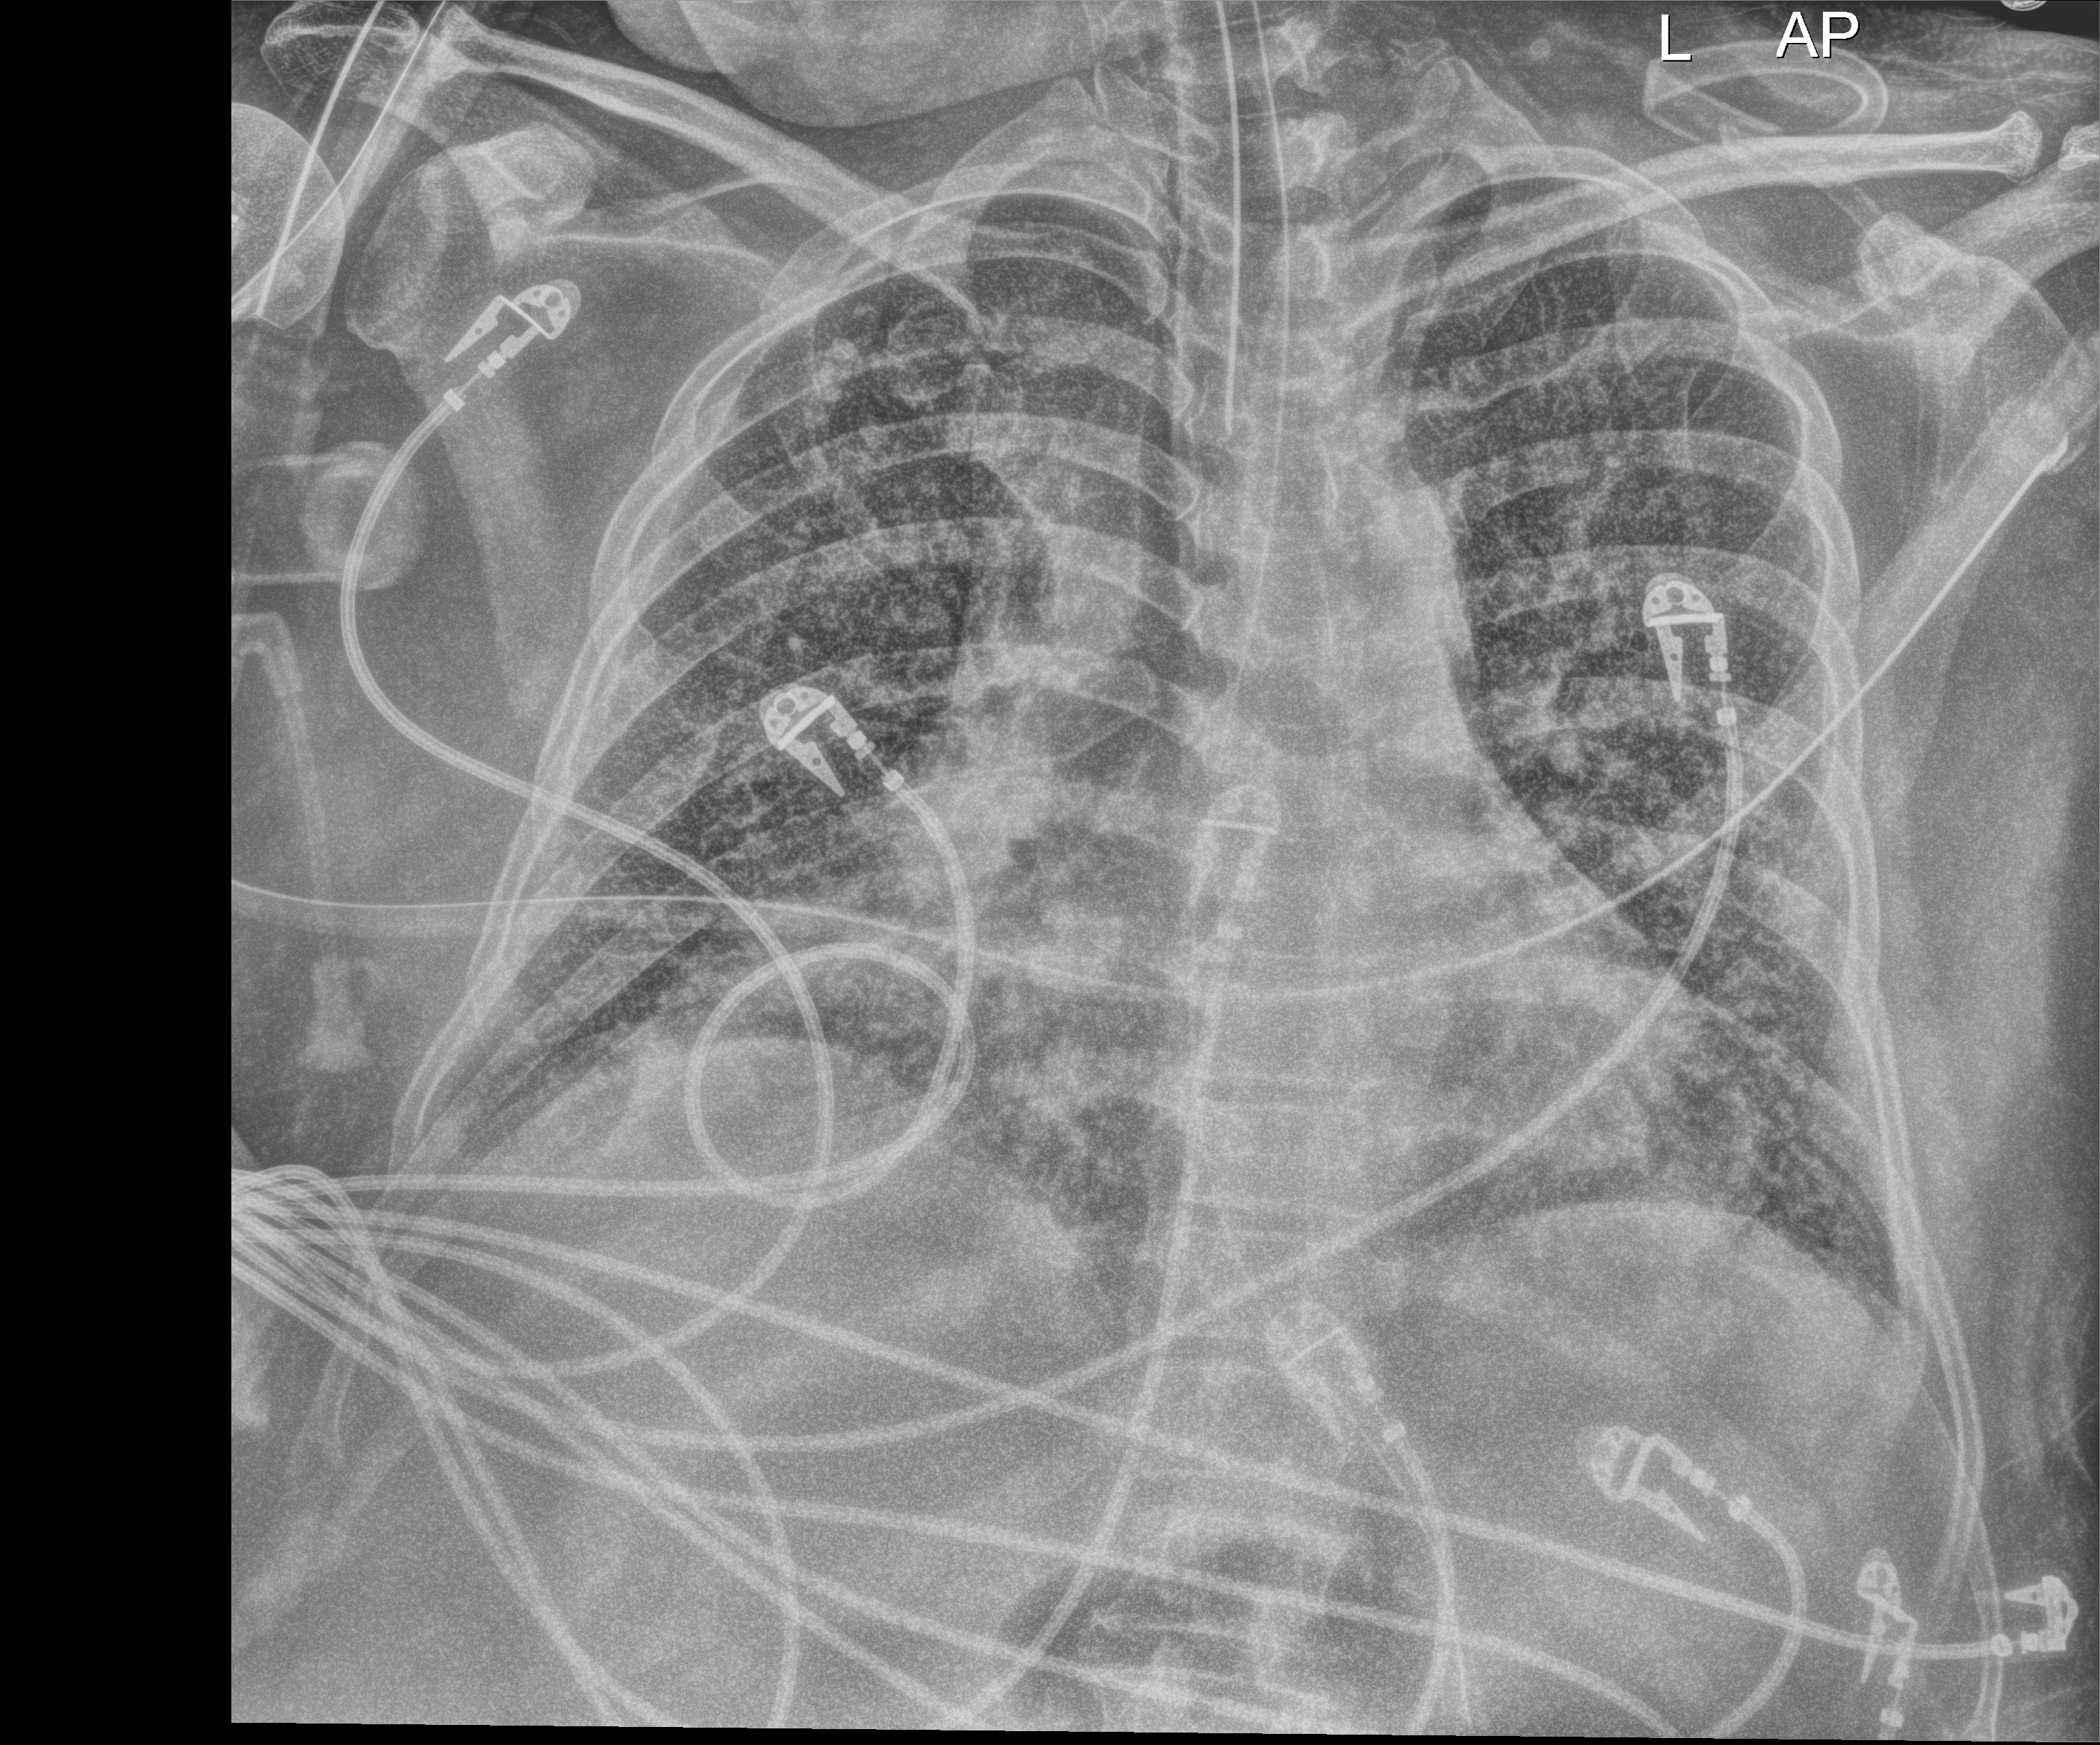
Chest X-ray (portable); anteroposterior (AP) projection. Patient hospitalised with COVID-19, aged 18–59 years.
Admission-level facts for this patient (not findings on this image; timing relative to this image not recorded):
- length of hospital stay: 48 days
- COPD (admission record): no